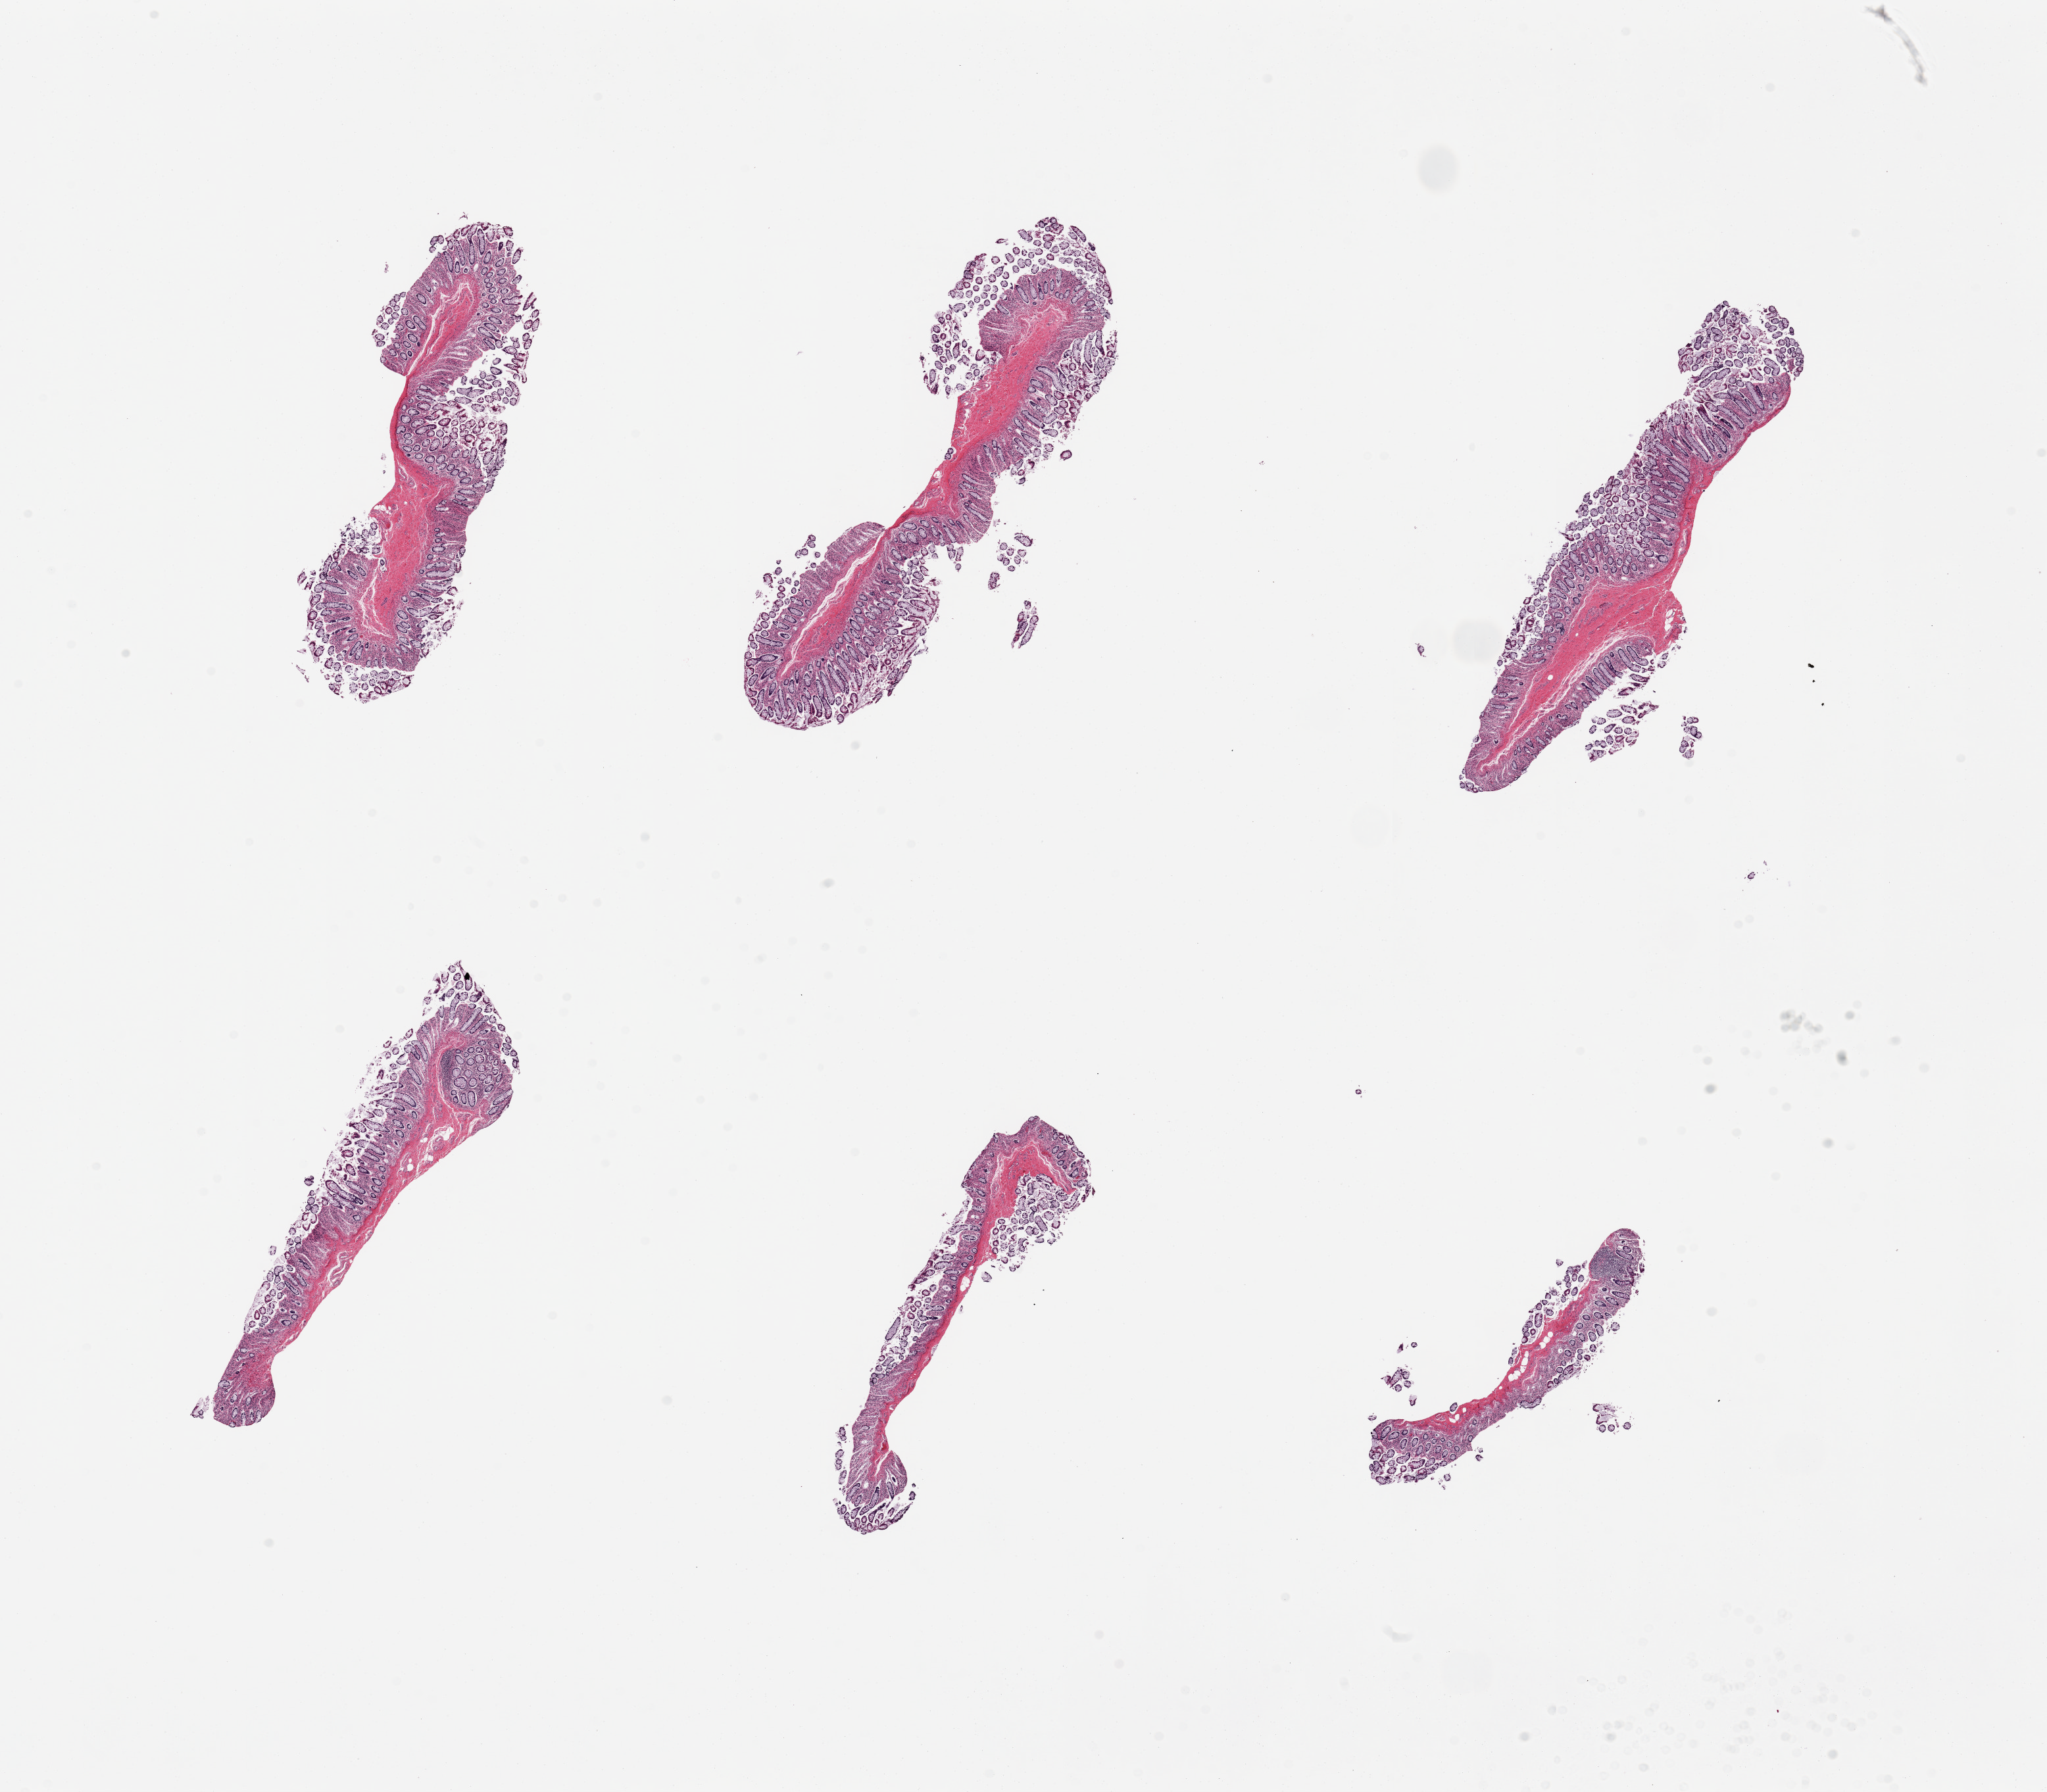
Whole-slide image, H&E stain — shown as a low-resolution overview of the whole scanned area (about 24.6 x 21.6 mm); PAXgene-fixed paraffin-embedded (PFPE) section; section of sigmoid colon (target tissue); donor tissue sample. Donor: female.
• reviewer comment on this tissue sample: 6 pieces, up to 7x3mm all colonic mucosa; 80-90% thickness is mucosa, moderately - severely autolyzed